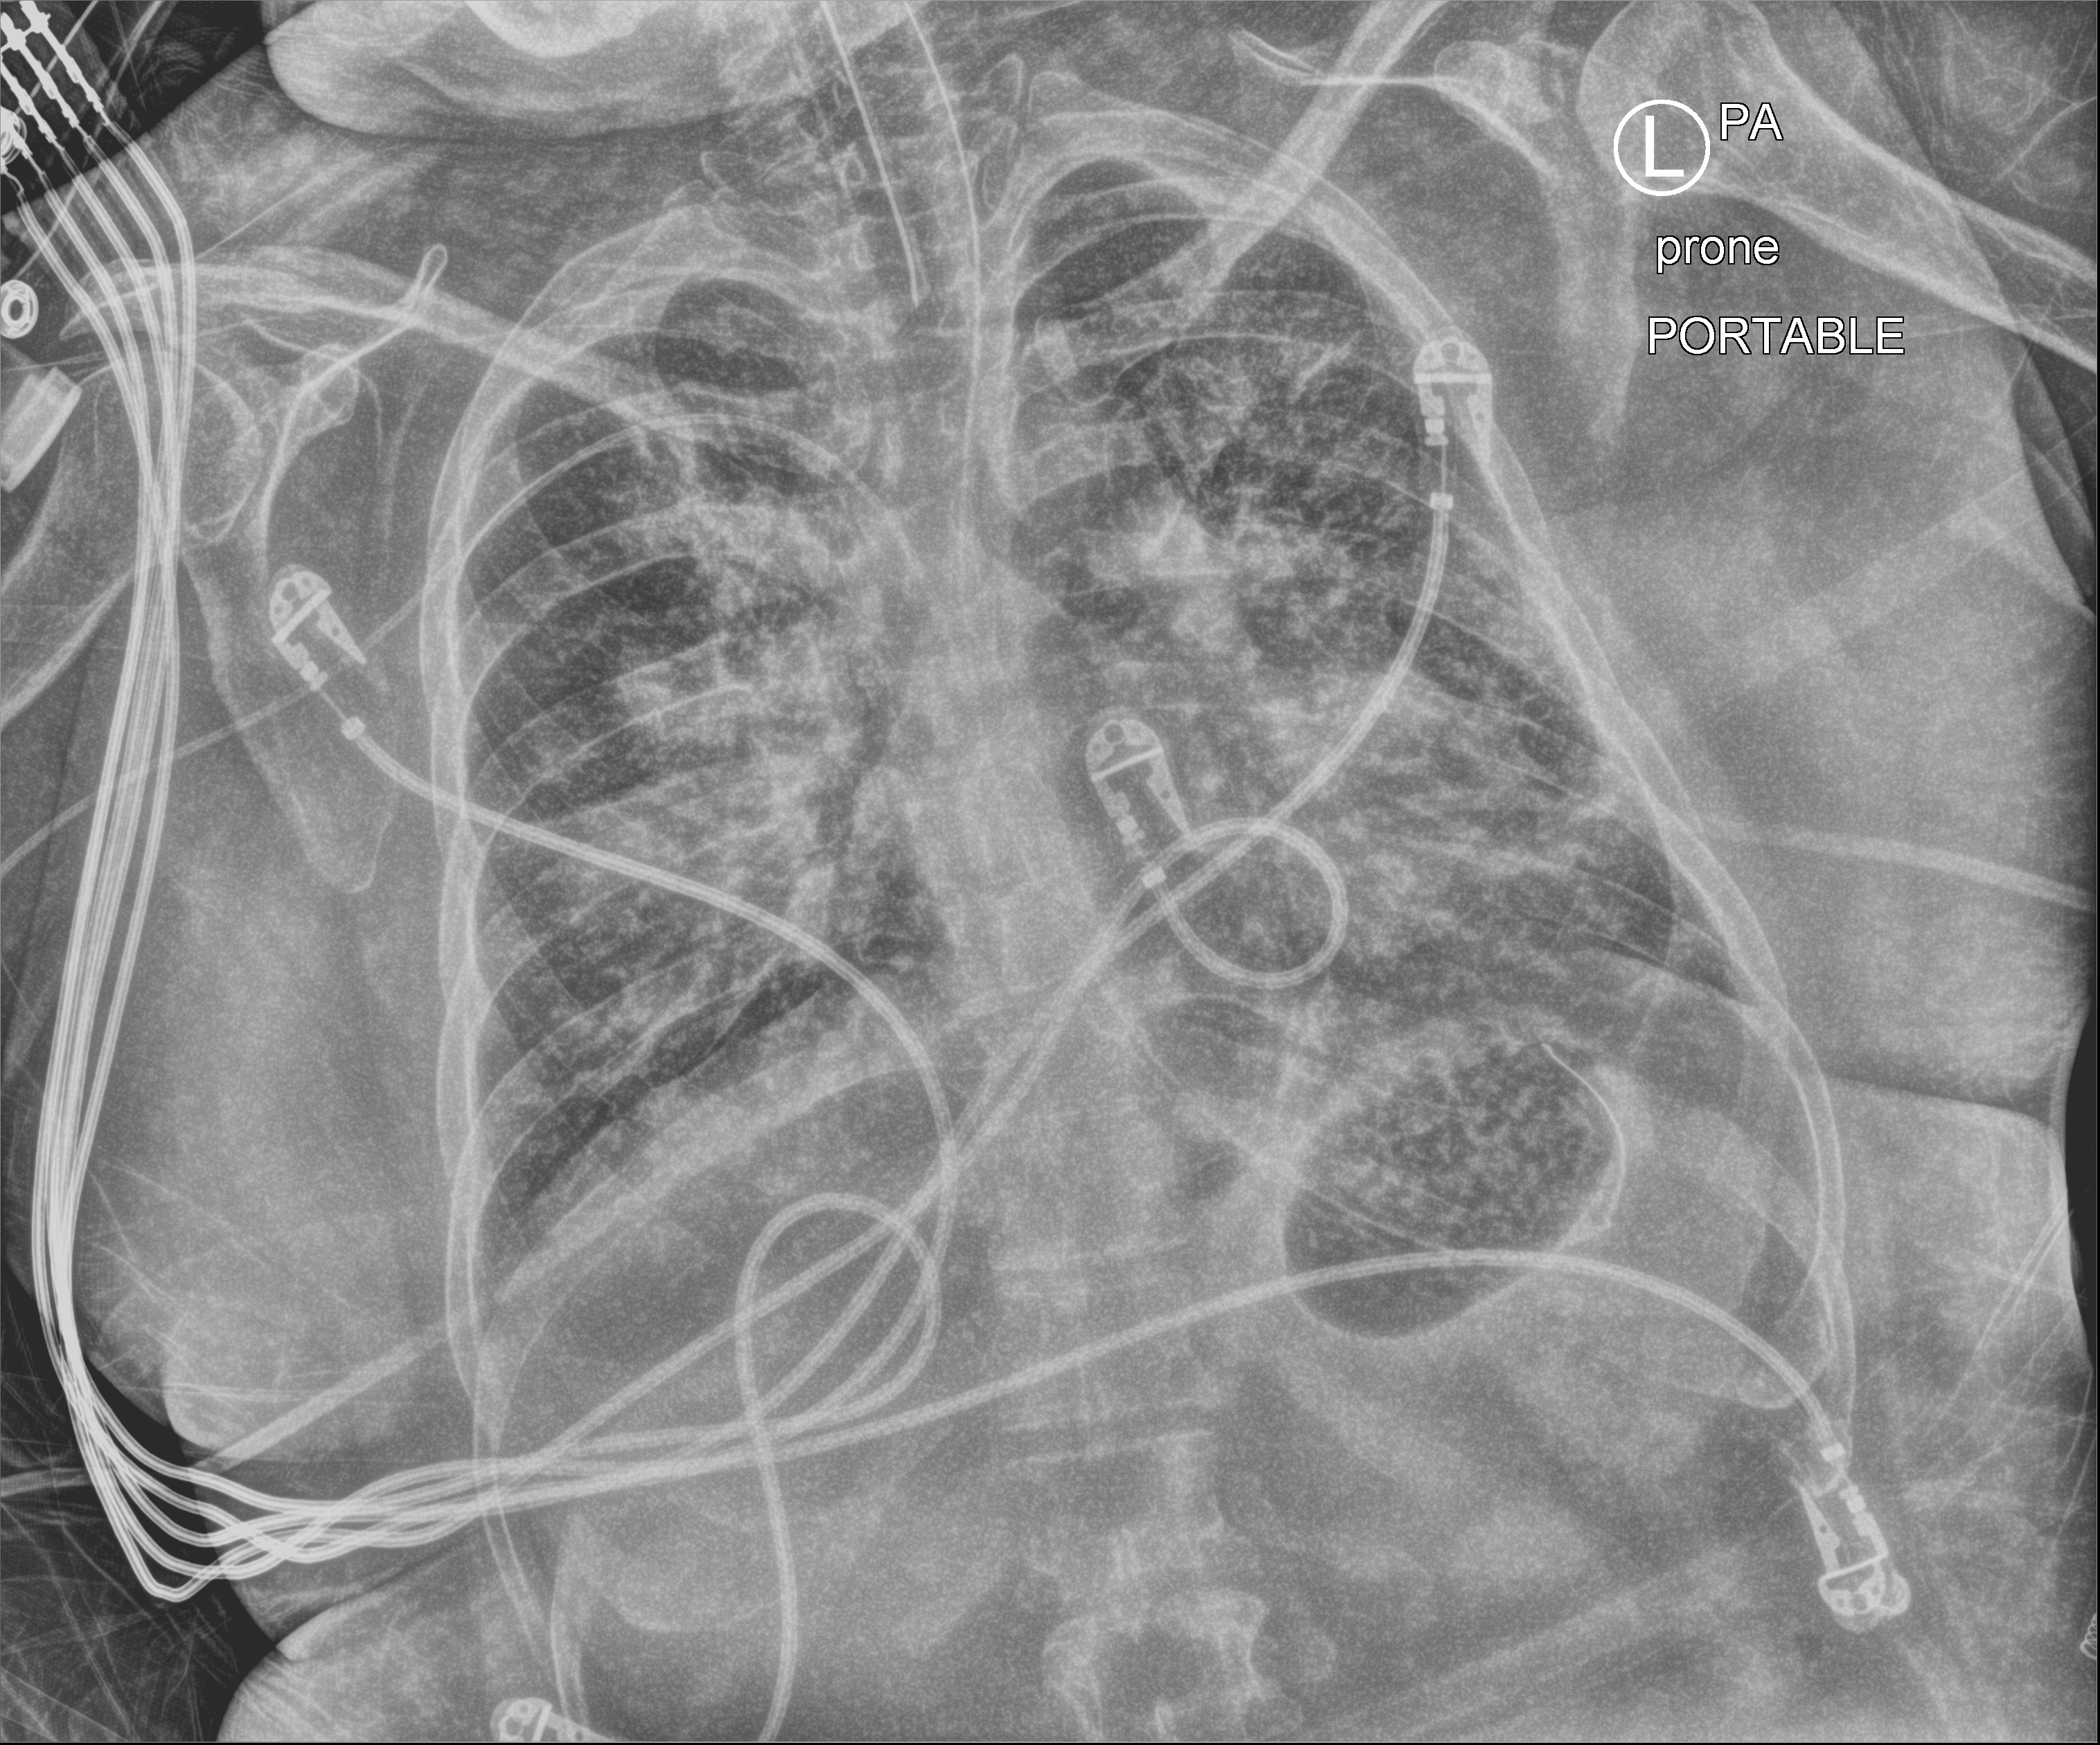
Chest radiograph; posteroanterior (PA) projection. Adult patient hospitalised with COVID-19, age 18–59 years.
From the hospital-stay record, not from the radiograph (when in the stay this image was taken is not recorded):
- admitted to intensive care during this hospital stay: yes